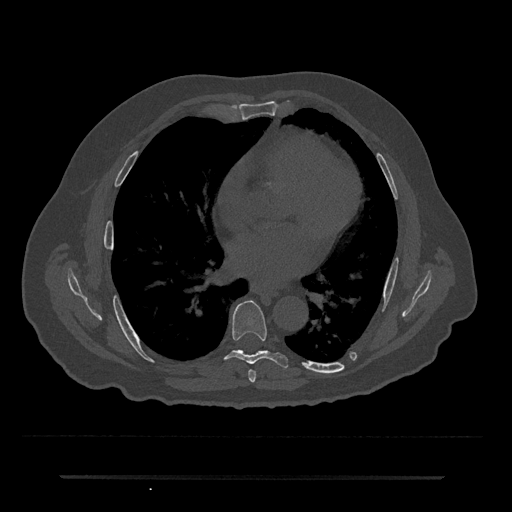
CT including the spine, one axial slice. Position 386 of 797 along the scan axis. 120 kVp. Bone window (W 1800 / L 400 HU). 0.5 mm slice thickness. 512 × 512 image matrix, field of view 437 × 437 mm. Patient: male, 69 years. Case-level facts recorded for this patient, not image findings: primary cancer: prostate.
Outlined on this slice (semi-automatic segmentation, software-assisted and operator-edited):
- T6 vertebra: box from (x=248, y=369) to (x=256, y=383) px
- T7 vertebra: (x=225, y=300)–(x=289, y=368)